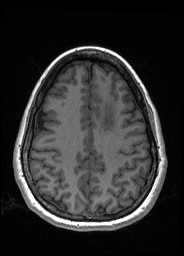
Pre-operative brain MRI before brain-tumour surgery, one axial slice. Position 61 of 176 along the scan axis. T1-weighted post-contrast. 1 mm slice thickness. 184 × 256 image matrix. From the clinical record (not read from this slice): histopathology: Oligodendroglioma; WHO grade: 2; IDH mutation: yes; tumour location: Left Frontal.
Structures marked on this image (expert manual segmentation):
- tumour: bounding box (x1, y1, x2, y2) in pixels: (100, 98, 117, 132)